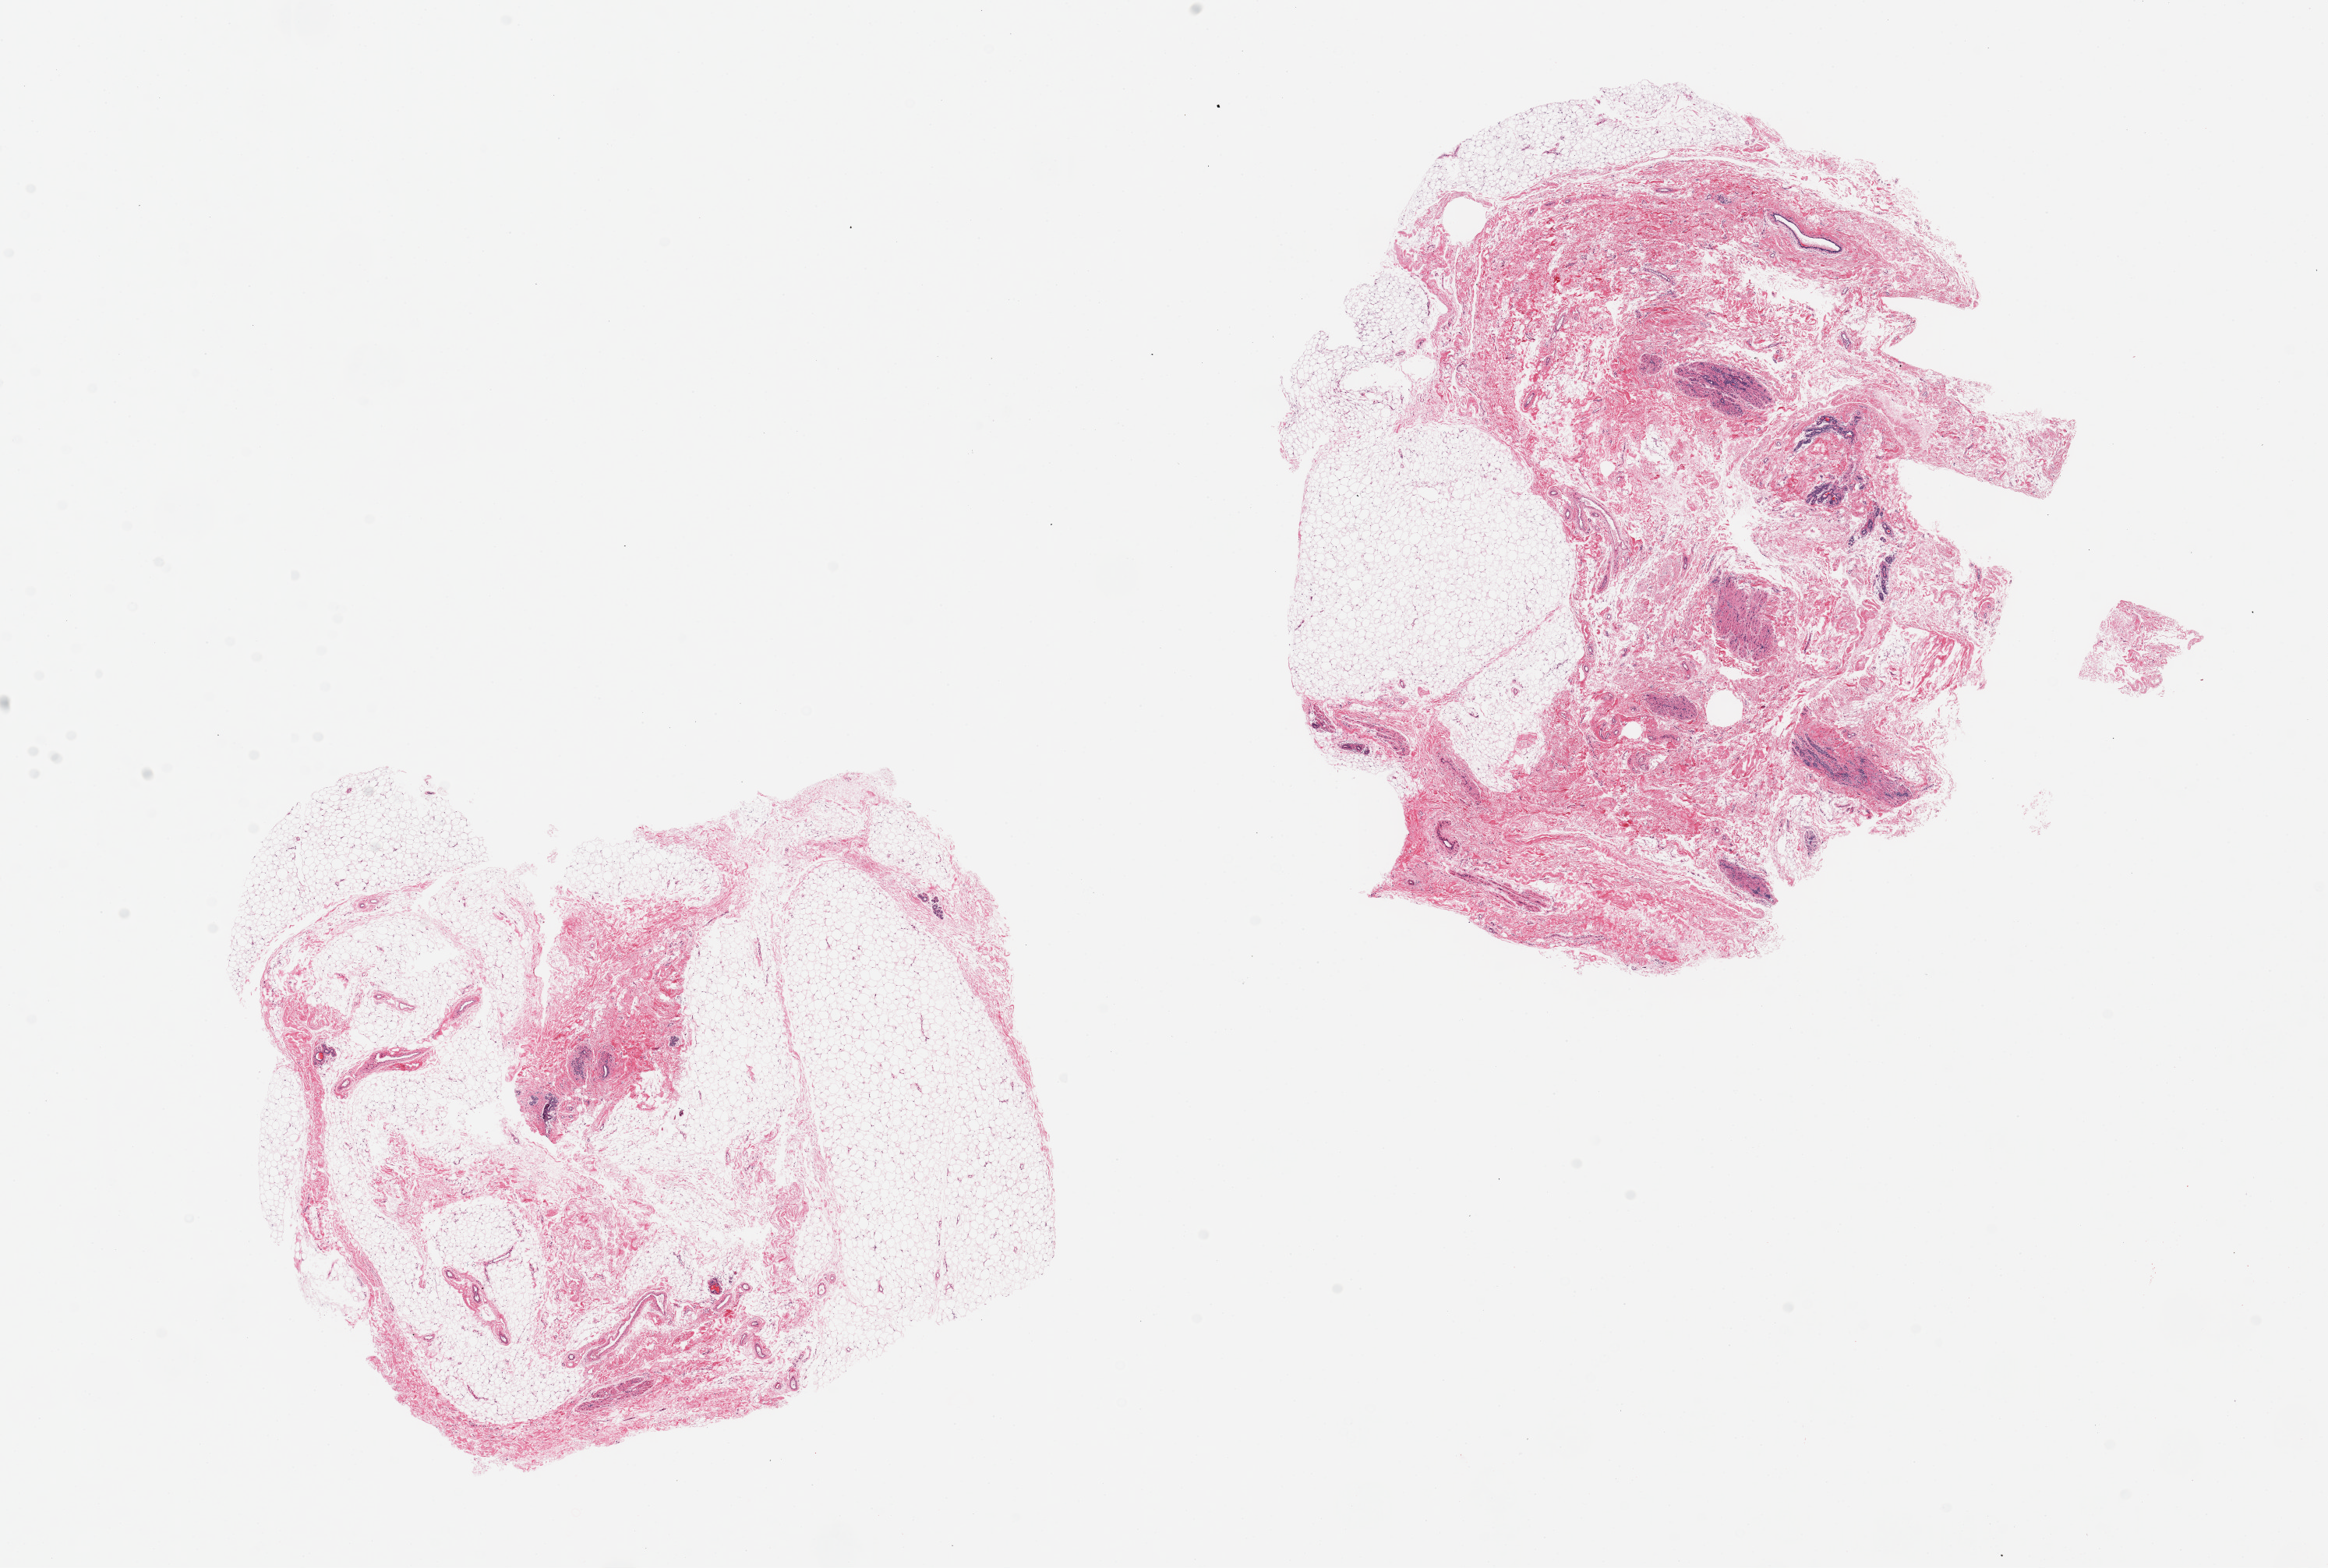
Hematoxylin and eosin (H&E) whole-slide image, brightfield — whole scanned area (about 23.6 x 15.9 mm, acquisition: 20x scan) shown as a low-resolution overview. PAXgene-fixed paraffin-embedded (PFPE) section. Target tissue: breast. Donor tissue sample. Donor: female.
Review note (as recorded): 2 pieces, 8x7 & 9x8mm; atrophic mammary lobules noted (rare) representatively.